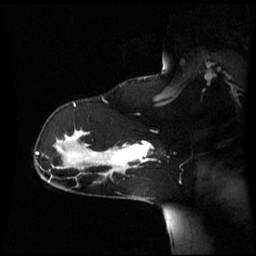
Breast MRI (dynamic contrast-enhanced), one sagittal slice; position 43 of 60 along the scan axis; dynamic contrast-enhanced series, image 2 of 3 at this slice position (ordered by acquisition); 1.5 T; TE 4.2 ms, TR 8.4 ms; 2.8 mm slice thickness; 256 × 256 image matrix, field of view 270 × 270 mm. Patient: female, 39 years. Case-level facts recorded for this patient, not image findings: setting: breast cancer imaged before/during neoadjuvant chemotherapy; receptor status: triple-negative.
Outlined on this slice (semi-automatic segmentation, software-assisted and operator-edited):
- analysis volume of interest (the breast-tissue region the enhancement analysis was run in; not a lesion): box from (x=101, y=143) to (x=150, y=173) px
- tumour enhancement mask (voxels above the 70 % enhancement threshold inside the analysis volume of interest): (x=112, y=143)–(x=149, y=165)